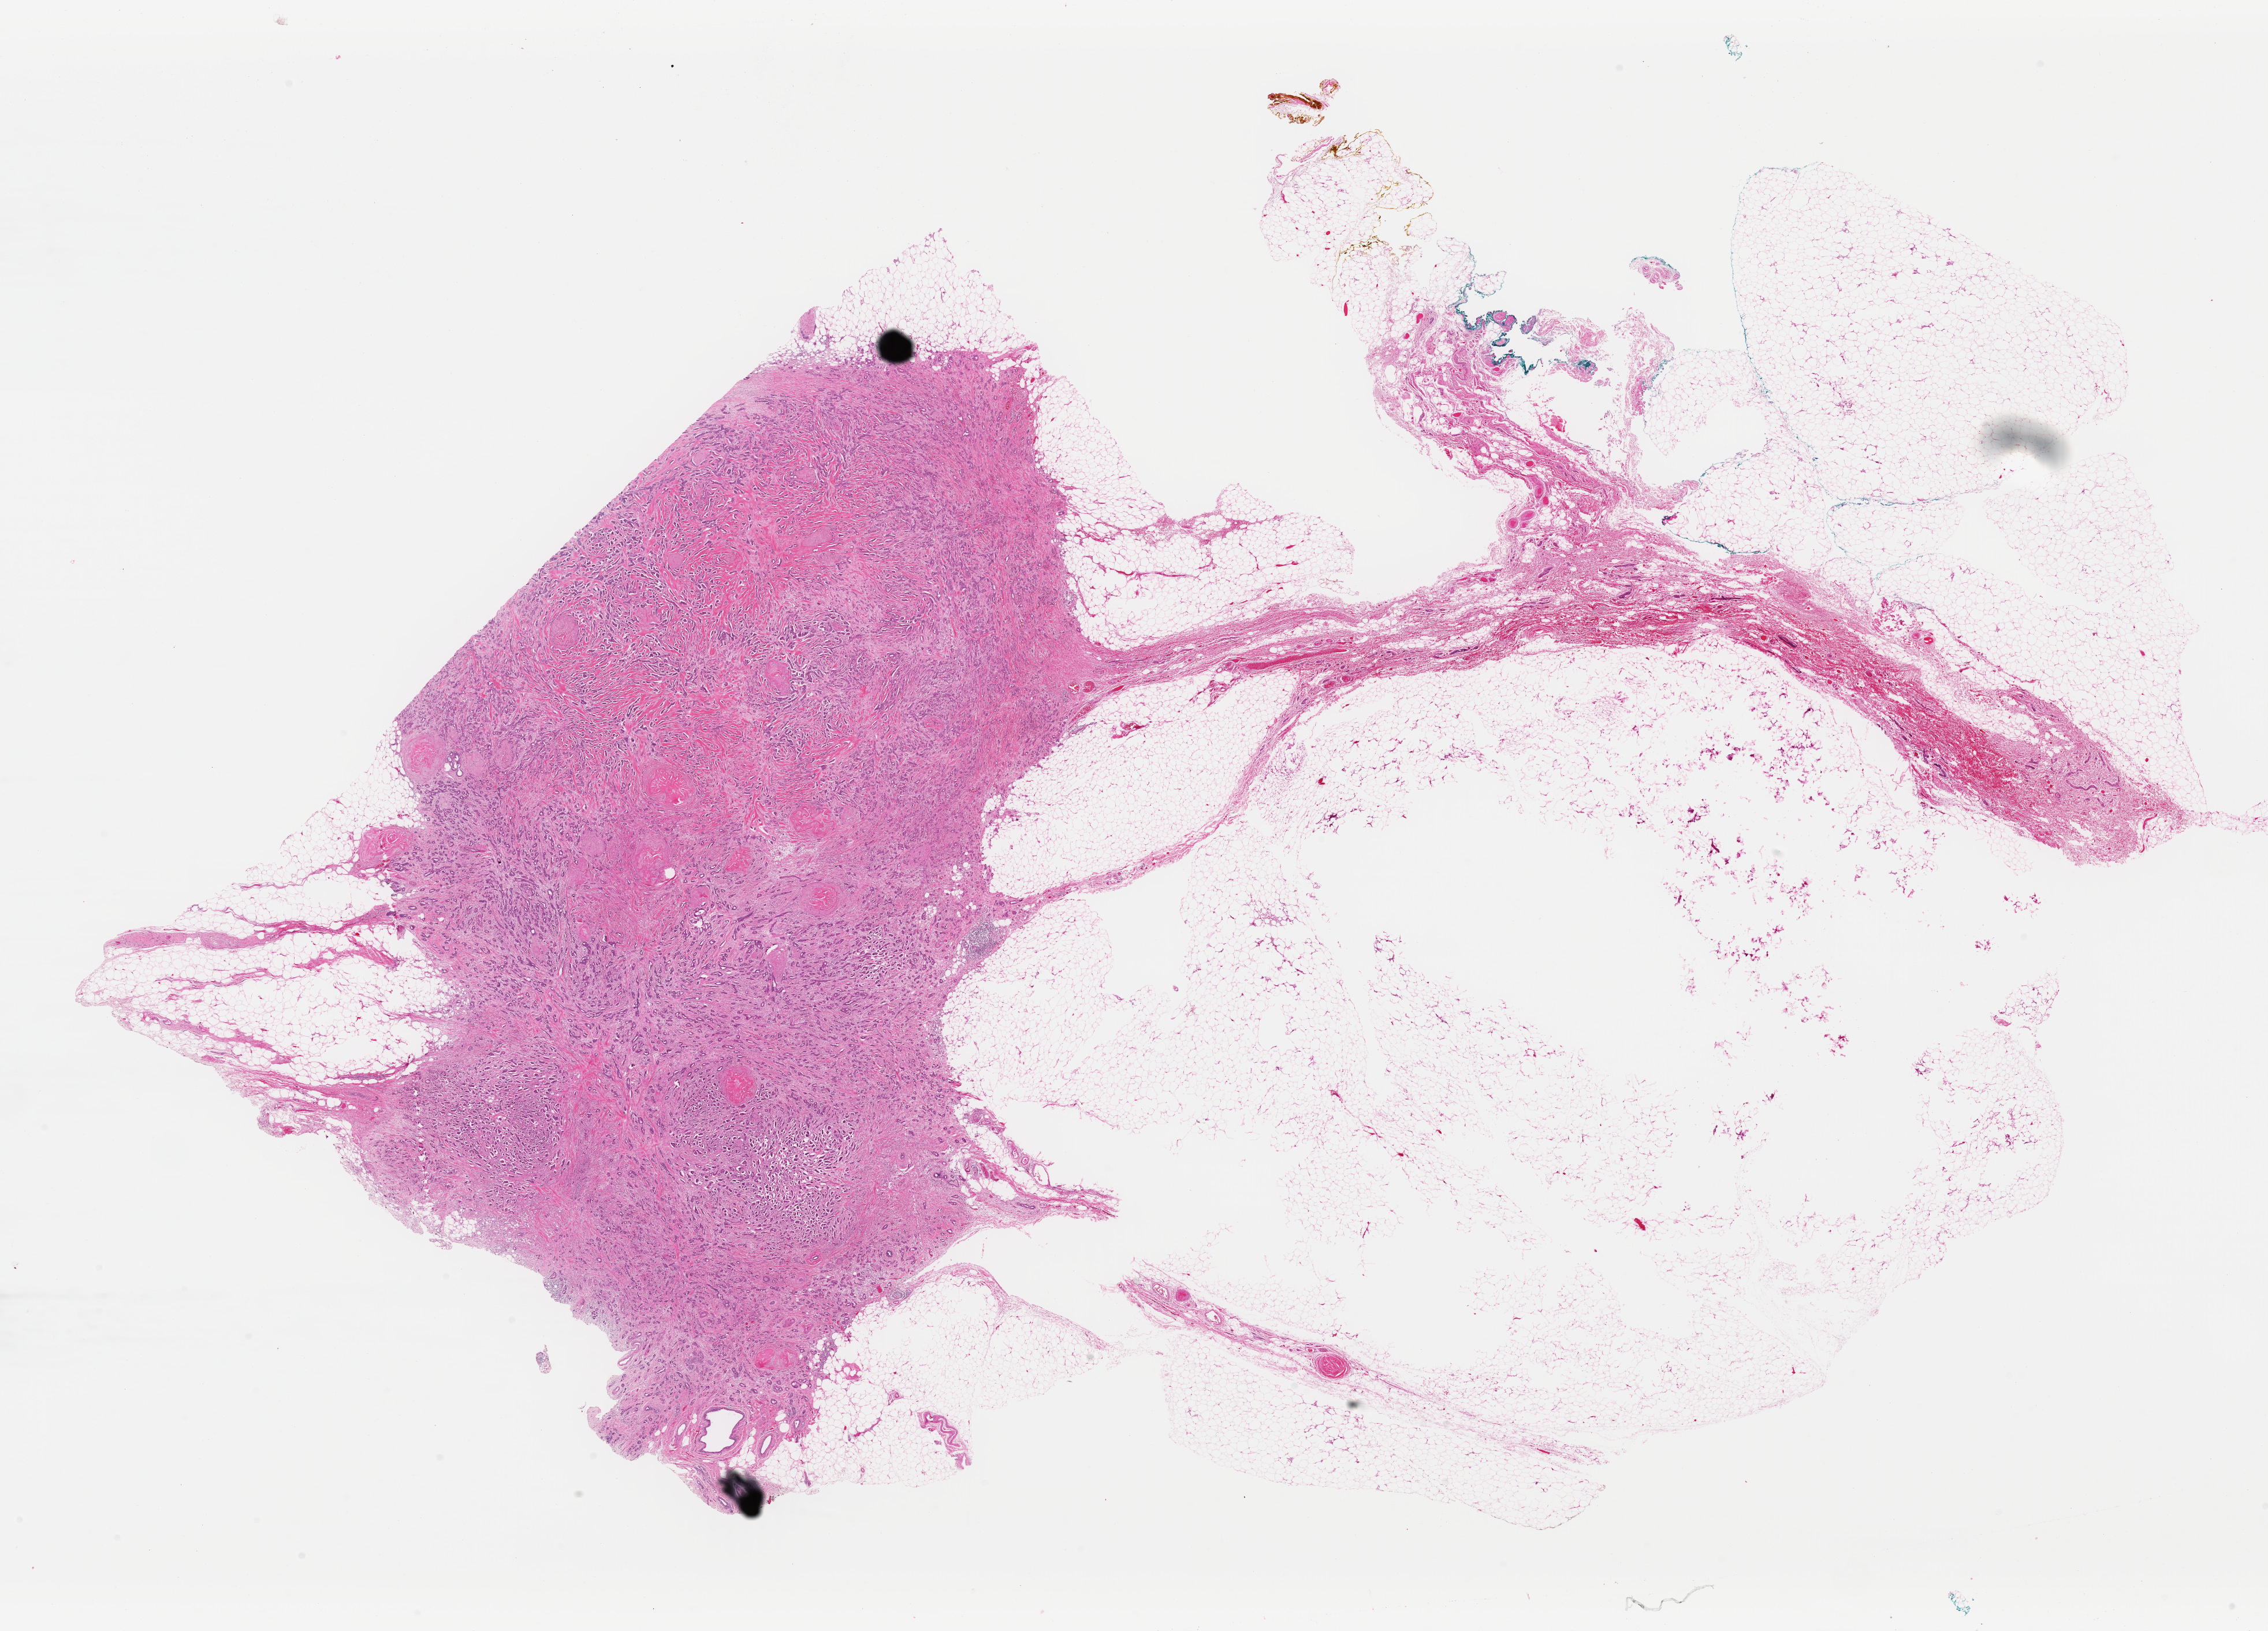
Whole-slide histology image, H&E-stained — a low-resolution overview of the entire scanned area, about 31.0 x 22.3 mm, FFPE section, sample: primary tumour, breast. Female patient; age at initial diagnosis 66 years.
Lymph nodes positive (case pathology): 0 of 6 examined. Laterality: right. AJCC pathologic stage: IA (5th edition). Diagnosis: Infiltrating duct carcinoma, NOS.